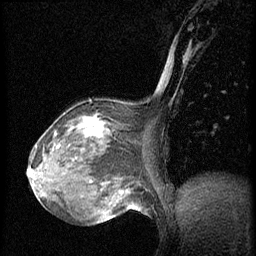
Breast MRI (dynamic contrast-enhanced), one sagittal slice. Slice 25 of 56 in the series (ordered by position). Dynamic contrast-enhanced series, image 2 of 3 at this slice position (ordered by acquisition). 1.5 T. TE 4.2 ms, TR 20.4 ms. 2 mm slice thickness. 256 × 256 image matrix, field of view 200 × 200 mm. Female patient, age 64 years. Case-level facts recorded for this patient, not image findings: setting: breast cancer imaged before/during neoadjuvant chemotherapy; receptor status: HR-positive, HER2-negative.
Outlined on this slice (semi-automatically segmented with operator editing):
- analysis volume of interest (the breast-tissue region the enhancement analysis was run in; not a lesion): bounding box <48,101,140,186> (left, top, right, bottom; pixels)
- tumour enhancement mask (voxels above the 70 % enhancement threshold inside the analysis volume of interest): <83,116,104,137>